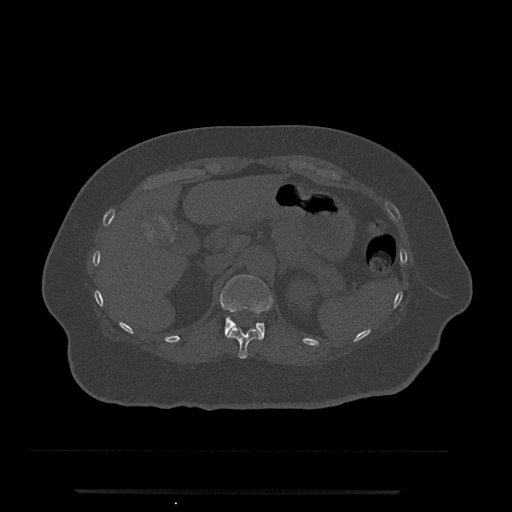
CT including the spine, one axial slice. Slice 198 of 797 in the series (ordered by position). 120 kVp. Bone window (W 1800 / L 400 HU). 512 × 512 image matrix. Female patient, age 51 years. From the clinical record (not read from this slice): primary cancer: neuro.
Outlined on this slice (semi-automatic segmentation, software-assisted and operator-edited):
- T11 vertebra: box from (x=226, y=327) to (x=261, y=359) px
- T12 vertebra: (x=220, y=275)–(x=273, y=341)